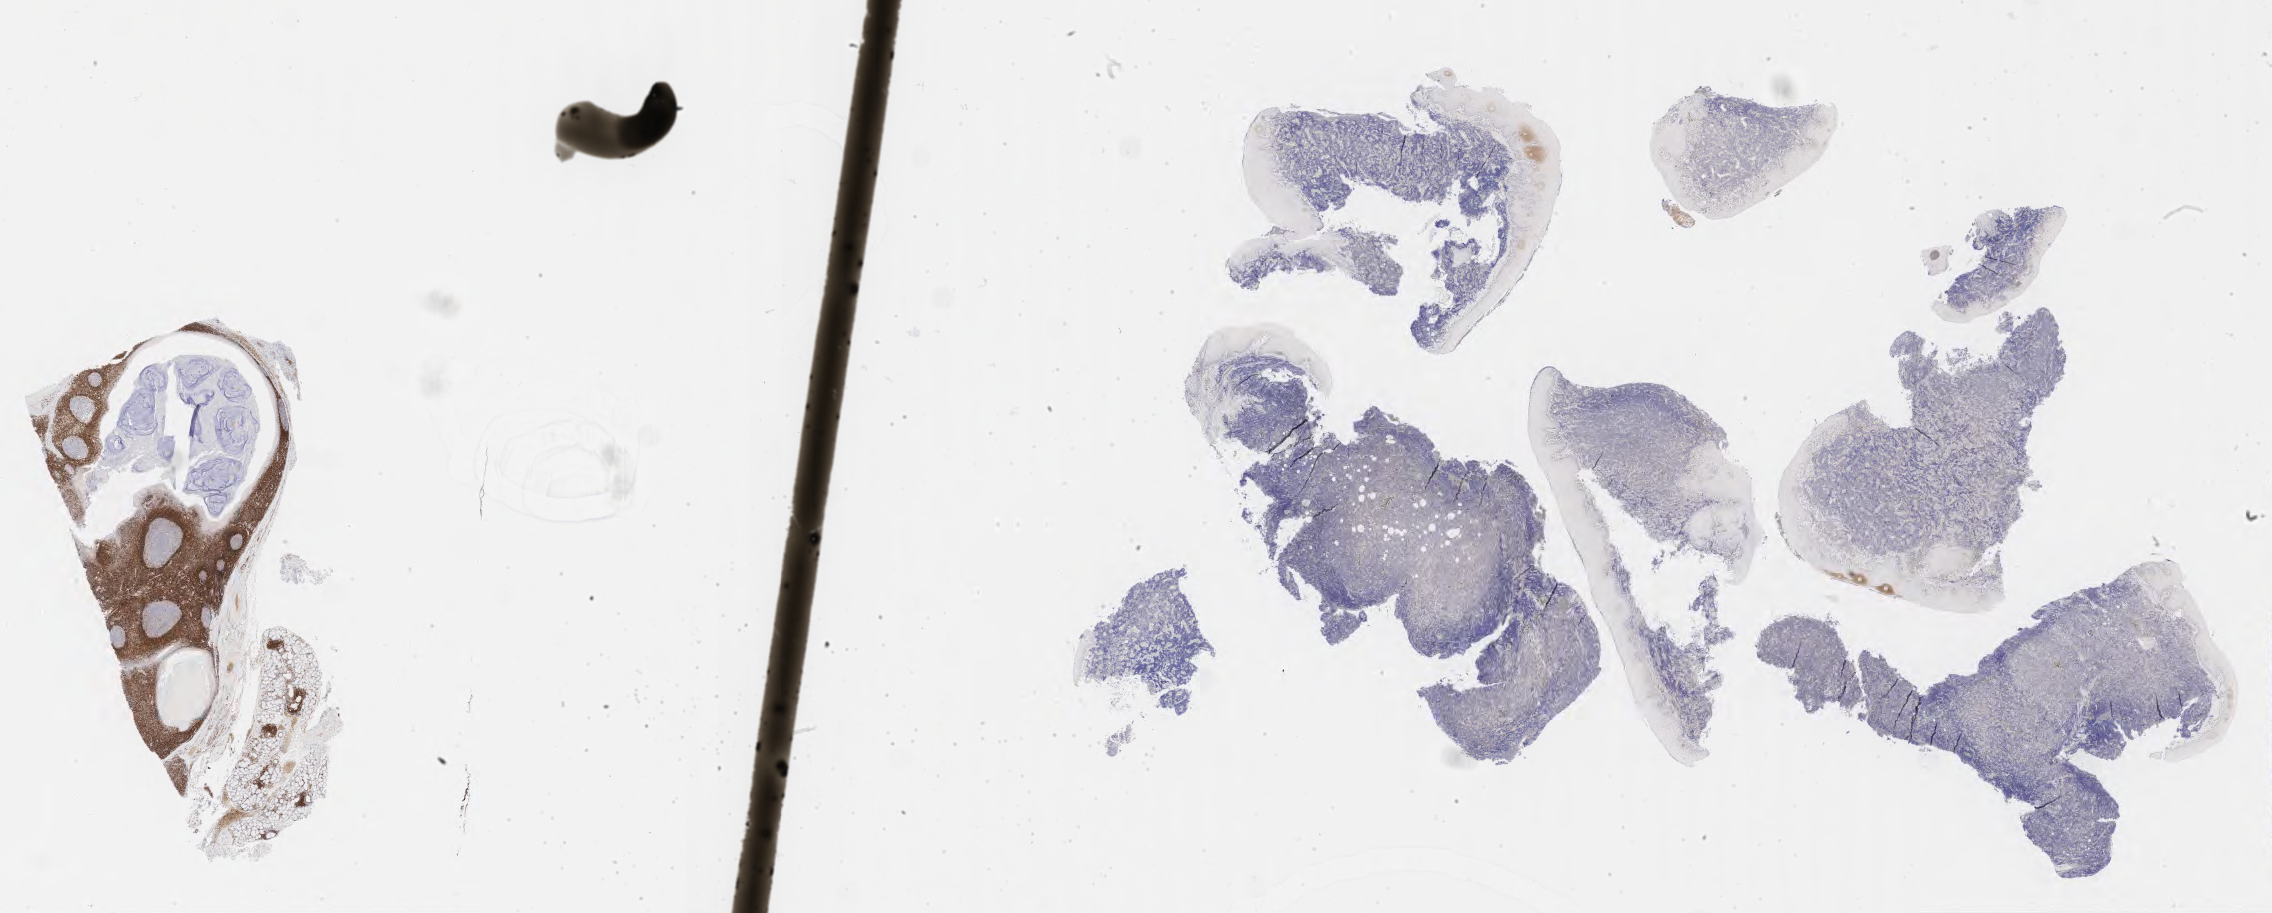
Whole-slide image, immunohistochemical stain for BCL2, shown as a low-resolution overview of the whole scanned area (about 36.7 x 14.8 mm). Tumor tissue. Patient male; aged 43.
Histologic diagnosis: Burkitt lymphoma, NOS.